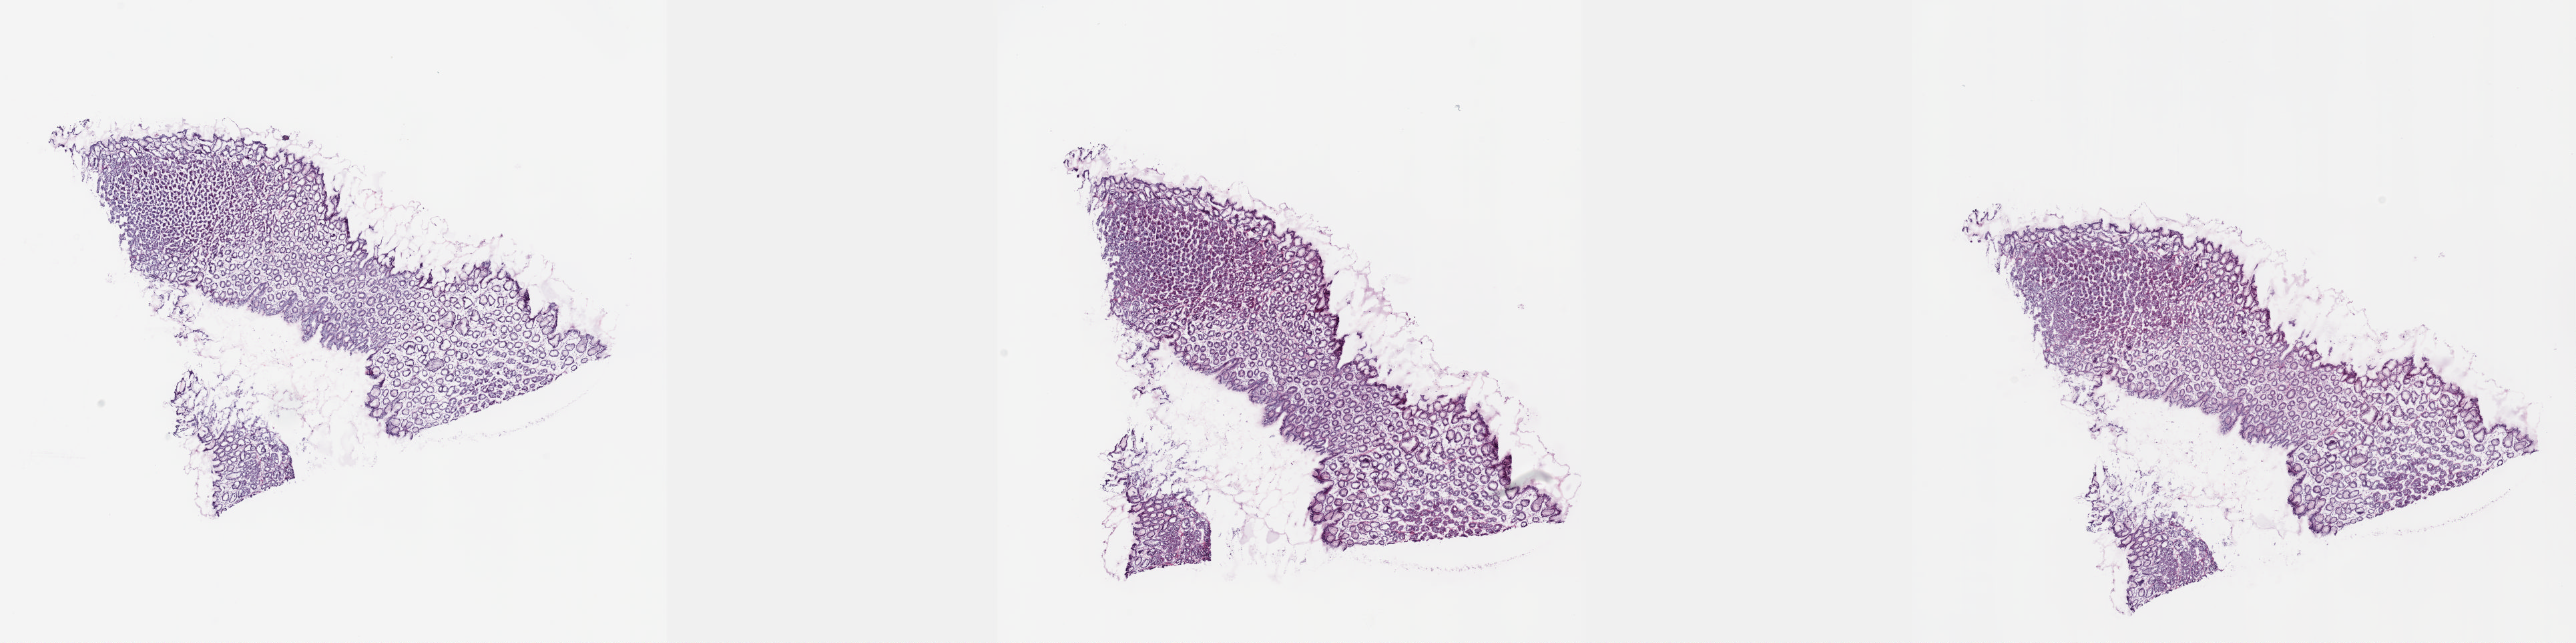
Whole-slide histology image, H&E-stained — whole scanned area (about 31.1 x 7.8 mm, from a 20x scan) shown as a low-resolution overview, frozen section from the top of the tissue portion, esophagus, solid tissue normal (non-tumour tissue) sample. Male patient; age at initial diagnosis 60 years. Pathologist review of this section (percent, as recorded): tumour cells 0%, tumour nuclei 0%, normal cells 100%, stromal cells 0%, necrosis 0%. Inflammatory infiltration, as recorded: lymphocyte infiltration 3%, monocyte infiltration 0%, neutrophil infiltration 0%.
• this section: solid tissue normal (non-tumour) sample from the same patient
• patient diagnosis: Adenocarcinoma, NOS